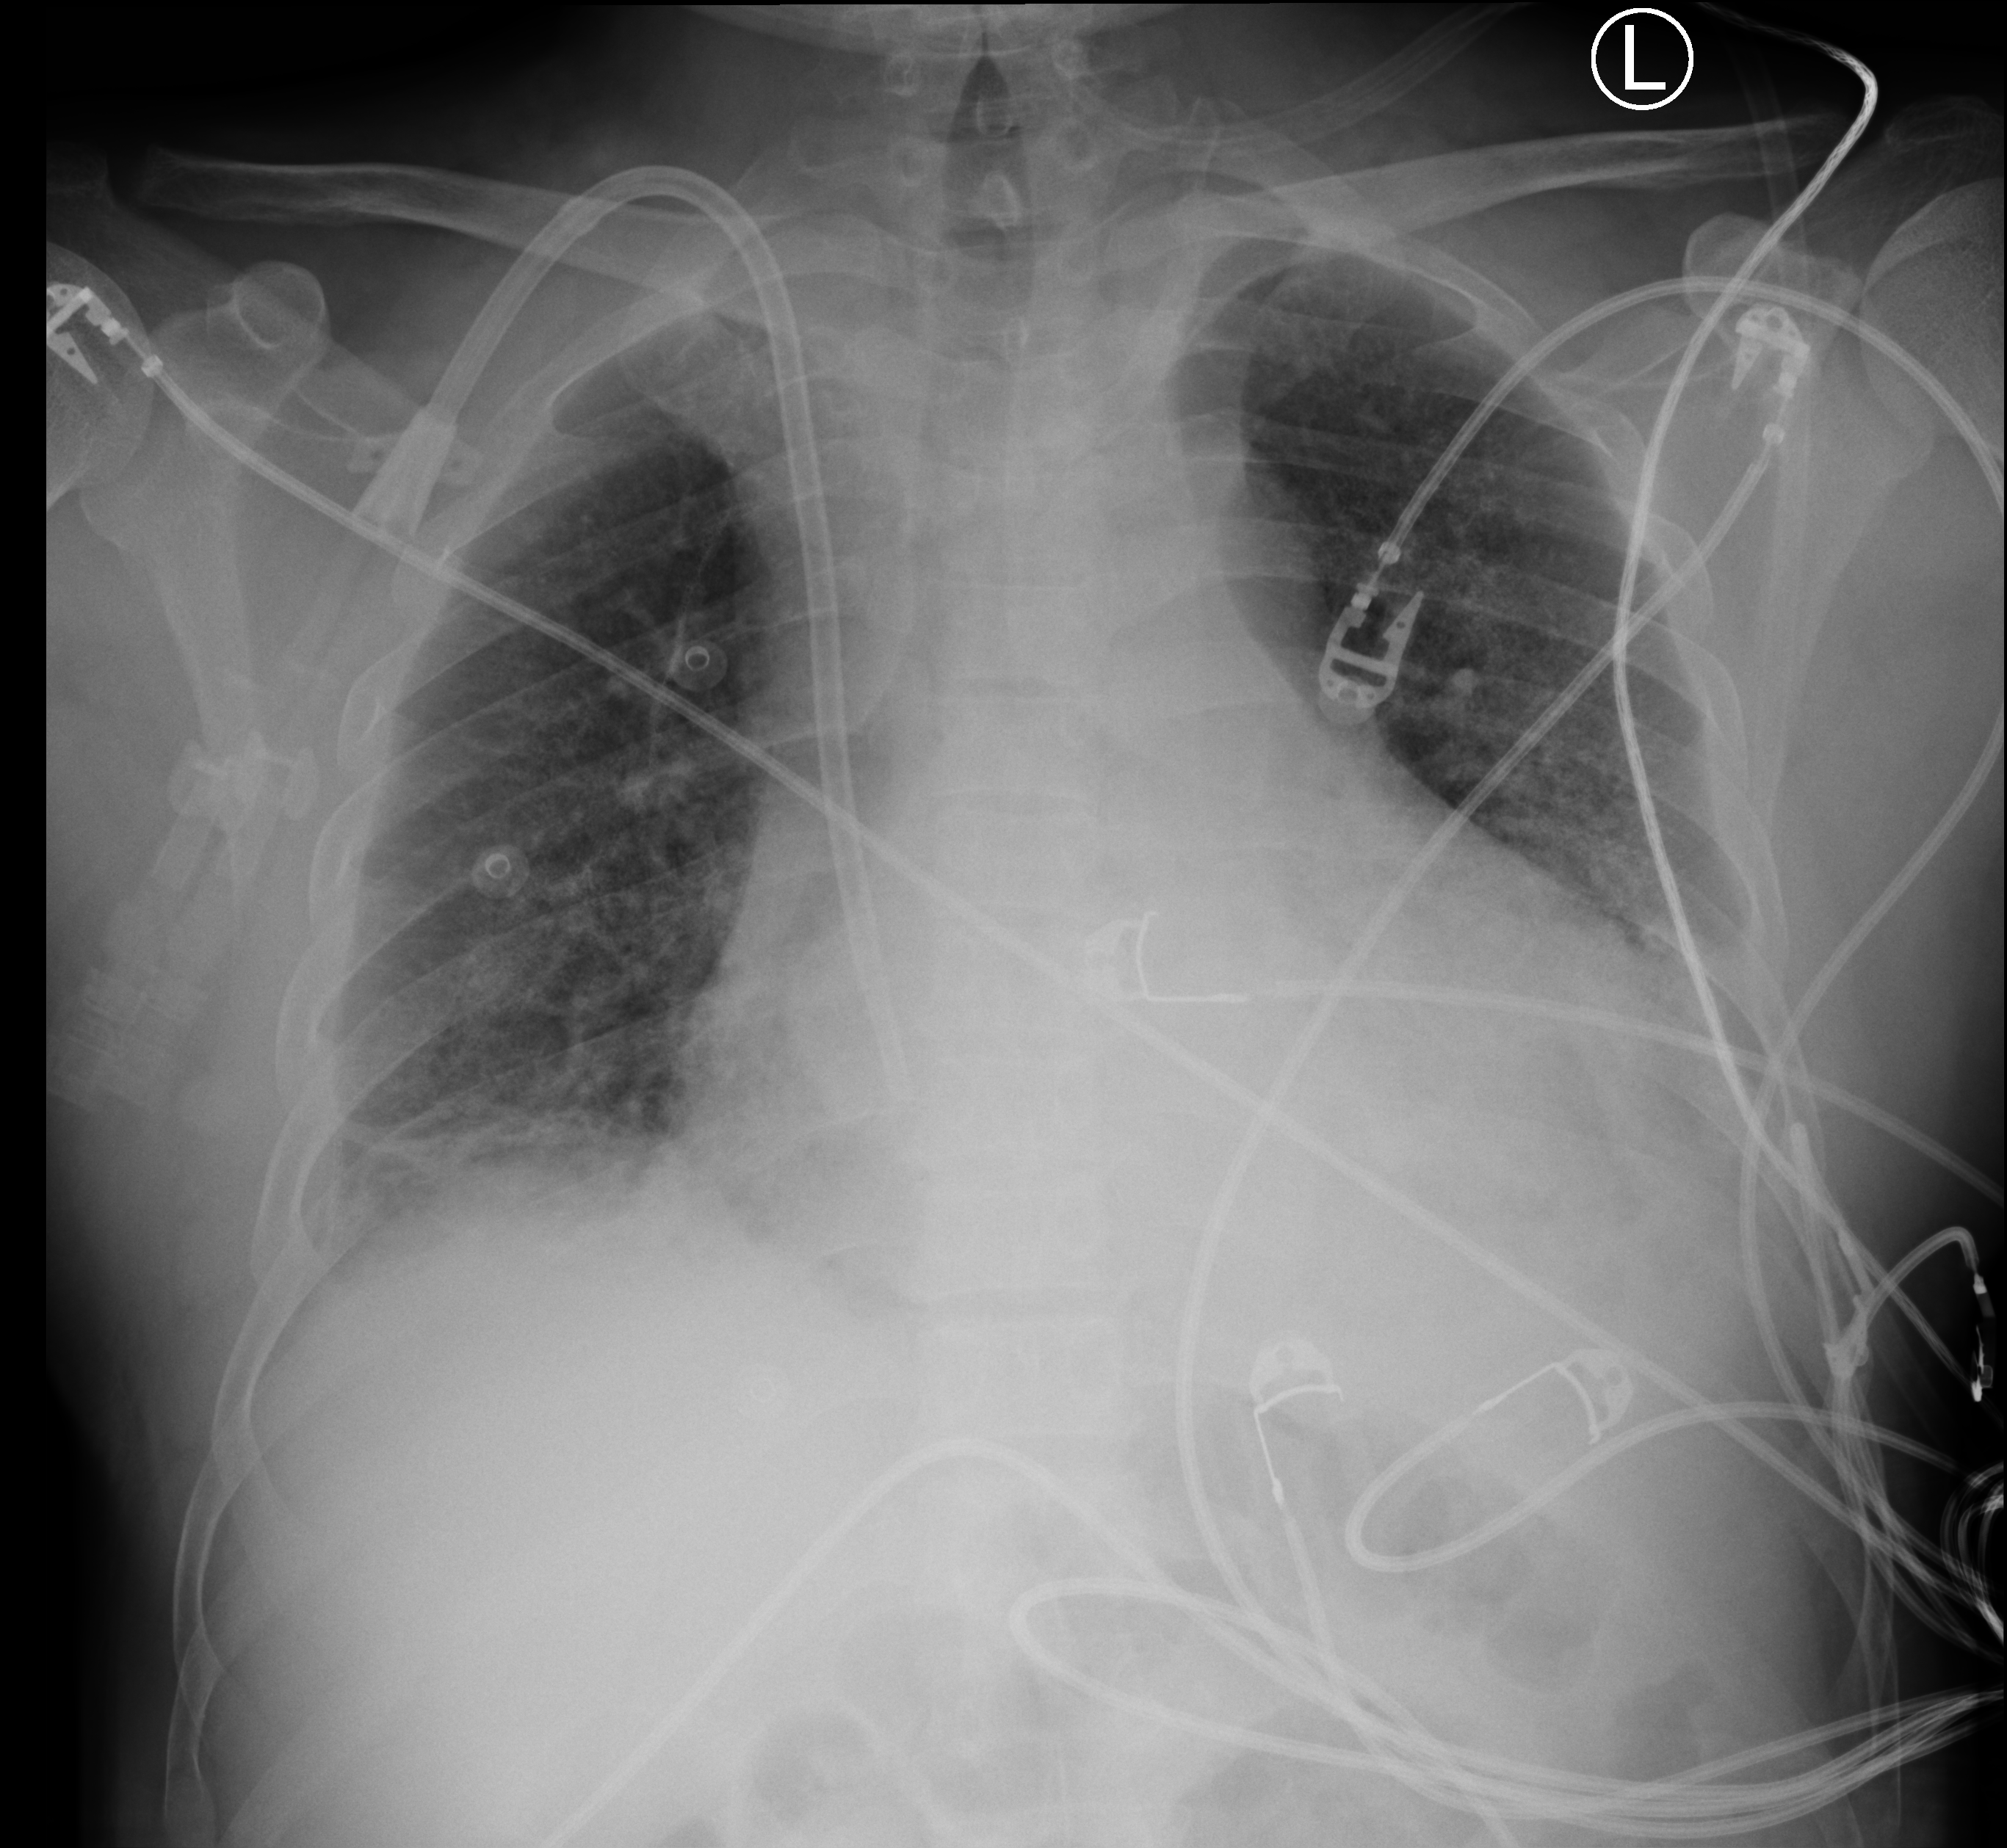
Bedside chest radiograph (computed radiography); anteroposterior (AP) projection. Patient hospitalised with COVID-19; male, aged 18–59 years.
From the hospital-stay record, not from the radiograph (when in the stay this image was taken is not recorded): mechanically ventilated during this hospital stay: no; admitted to intensive care during this hospital stay: no; length of hospital stay: 7 days.